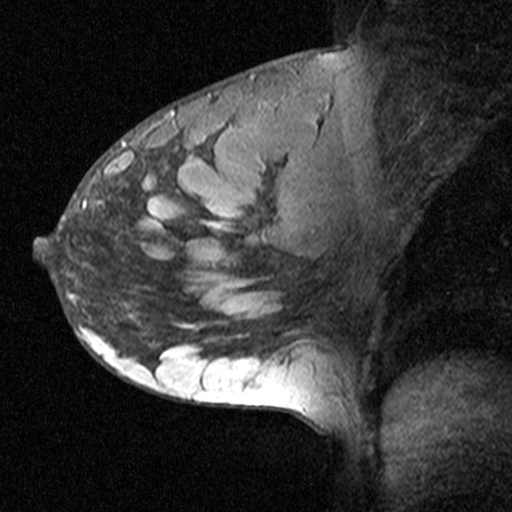
Breast MRI (dynamic contrast-enhanced), one sagittal slice; position 26 of 44 along the scan axis; dynamic contrast-enhanced study with each time point stored as its own series, time point 2 of 3 at this slice position (early post-contrast, ordered by acquisition time); 1.5 T; TE 4.5 ms, TR 11 ms; 3 mm slice thickness; 512 × 512 image matrix. Female patient, age 27 years. Case-level facts recorded for this patient, not image findings: setting: breast cancer imaged before/during neoadjuvant chemotherapy; receptor status: HR-positive, HER2-negative.
Annotated regions visible in this slice (semi-automatically segmented with operator editing):
- analysis volume of interest (the breast-tissue region the enhancement analysis was run in; not a lesion): bounding box (x1, y1, x2, y2) in pixels: (37, 162, 163, 271)
- tumour enhancement mask (voxels above the 90 % enhancement threshold inside the analysis volume of interest): (41, 199, 86, 241)